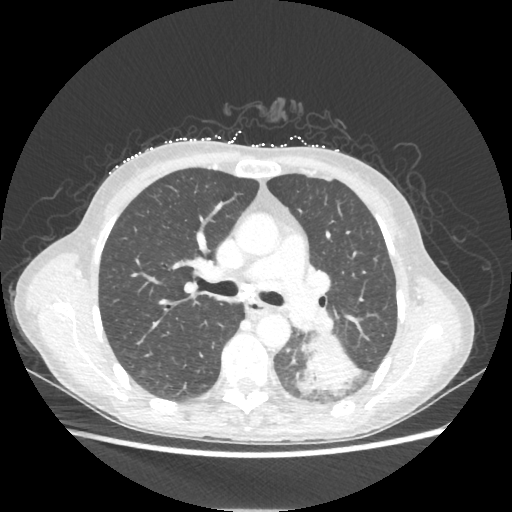
Chest CT, one axial slice; slice 135 of 221 in the series (ordered by position); 80 kVp; lung window (W 1500 / L -600 HU); 1.25 mm slice thickness; 512 × 512 image matrix. Patient: female, 53 years. Case-level facts recorded for this patient, not image findings: clinical TNM (as recorded): T3 N0 M0.
Structures marked on this image (bounding box drawn by a radiologist):
- lung tumour (recorded histology: adenocarcinoma): bounding box (x1, y1, x2, y2) in pixels: (302, 336, 362, 393)